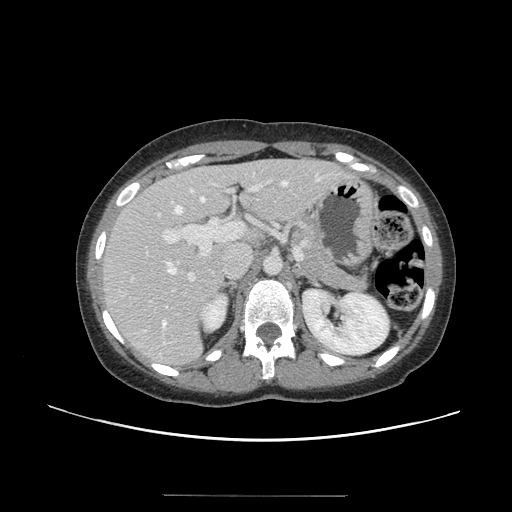
Contrast-enhanced abdominal CT, one axial slice. Position 87 of 144 along the scan axis. 120 kVp. Intravenous contrast given. Soft-tissue window (W 400 / L 40 HU). 2.5 mm slice thickness. 512 × 512 image matrix. Female patient, age 53 years. Case-level facts recorded for this patient, not image findings: diagnosis: colorectal cancer liver metastases, imaged before liver resection; multiple liver metastases: yes; largest metastasis: 1.1 cm; disease in both lobes: no.
Structures marked on this image (manually delineated by an expert):
- hepatic veins: bounding box (x1, y1, x2, y2) in pixels: (163, 179, 319, 327)
- liver: (103, 160, 349, 366)
- planned liver remnant (the part of the liver to remain after resection): (104, 160, 314, 297)
- portal vein (with intrahepatic branches): (130, 180, 301, 282)